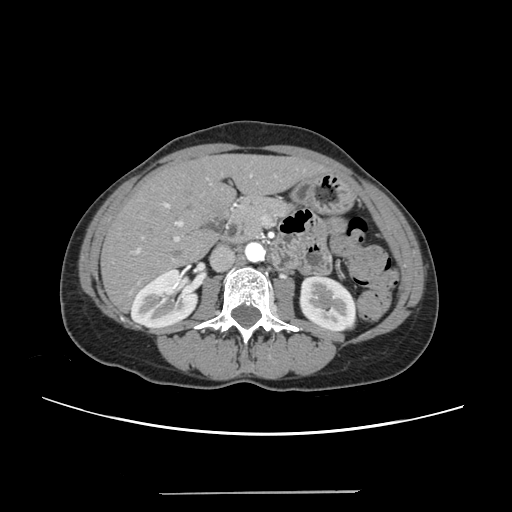
Contrast-enhanced abdominal CT, one axial slice. Position 109 of 240 along the scan axis. 120 kVp. Intravenous contrast given. Soft-tissue window (W 400 / L 40 HU). 1.25 mm slice thickness. 512 × 512 image matrix, field of view 371 × 371 mm. Female patient, age 60 years. Case-level facts recorded for this patient, not image findings: diagnosis: colorectal cancer liver metastases, imaged before liver resection; multiple liver metastases: no; largest metastasis: 1.5 cm; chemotherapy before resection: yes.
Annotated regions visible in this slice (manually delineated by an expert):
- liver: bounding box (x1, y1, x2, y2) in pixels: (103, 156, 321, 308)
- planned liver remnant (the part of the liver to remain after resection): (103, 157, 321, 308)
- portal vein (with intrahepatic branches): (132, 174, 252, 253)